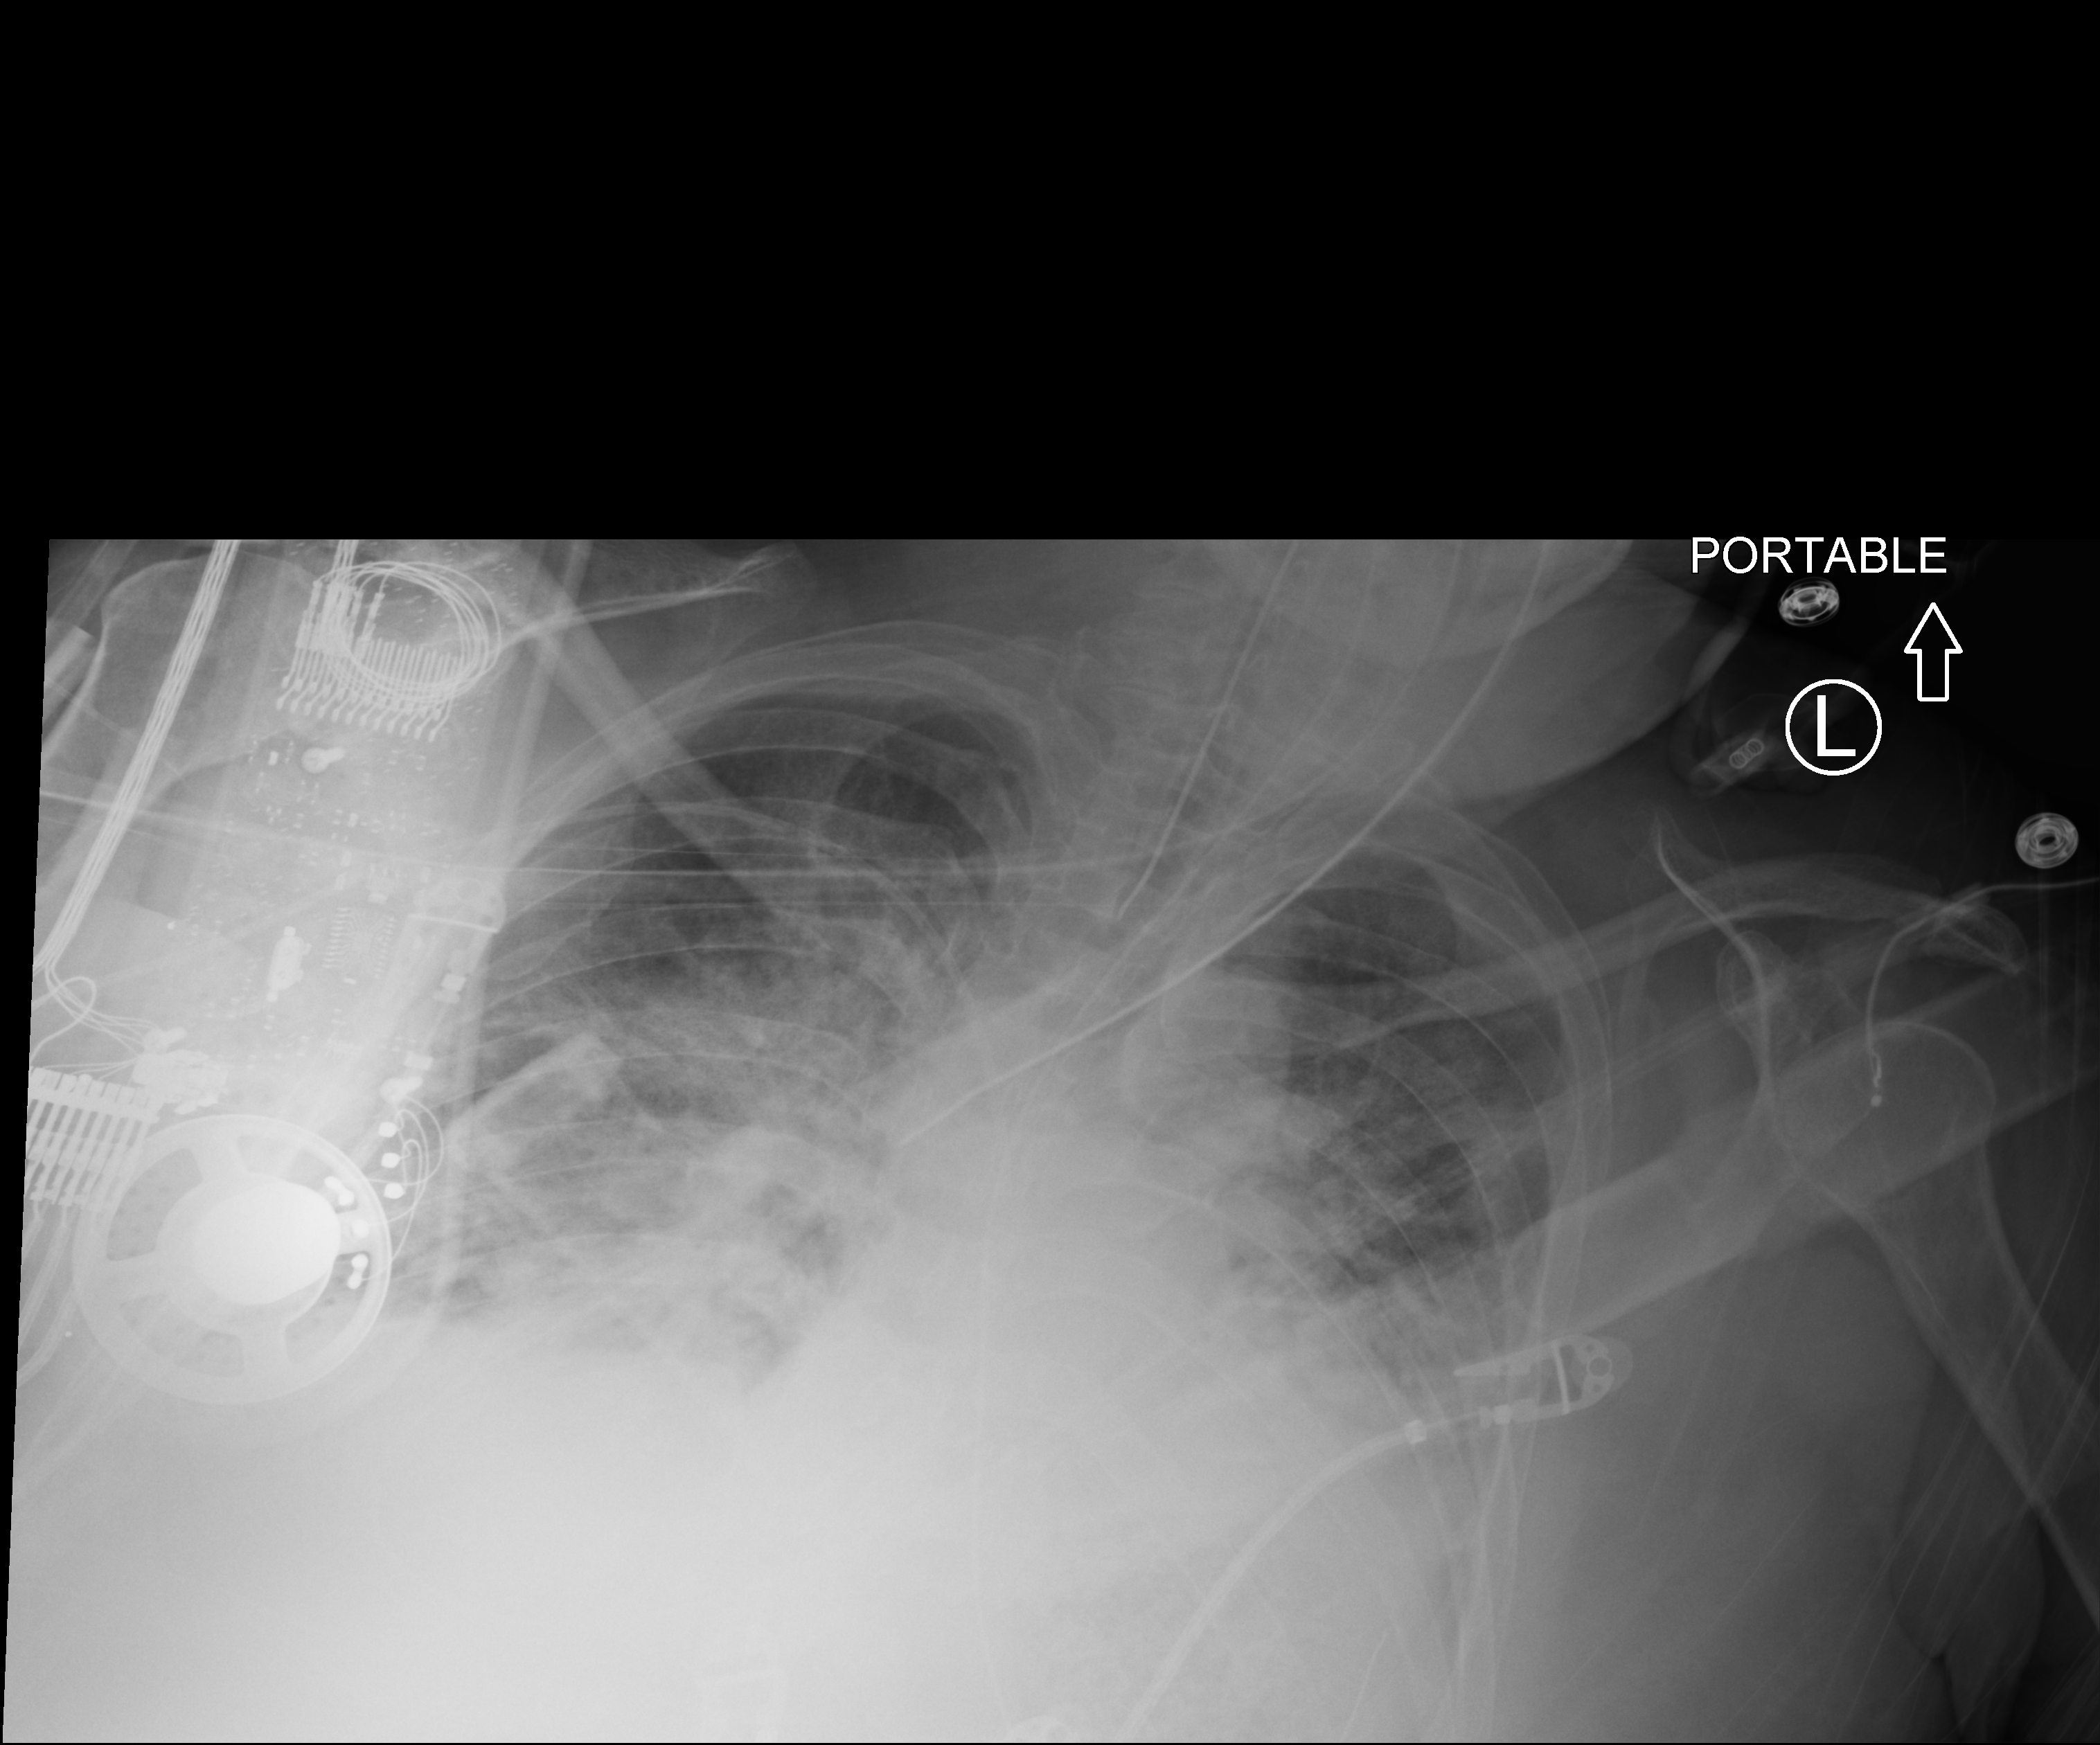
Portable chest radiograph; anteroposterior (AP) projection. Patient hospitalised with COVID-19, aged 18–59 years.
From the hospital-stay record, not from the radiograph (when in the stay this image was taken is not recorded): admitted to intensive care during this hospital stay: yes.